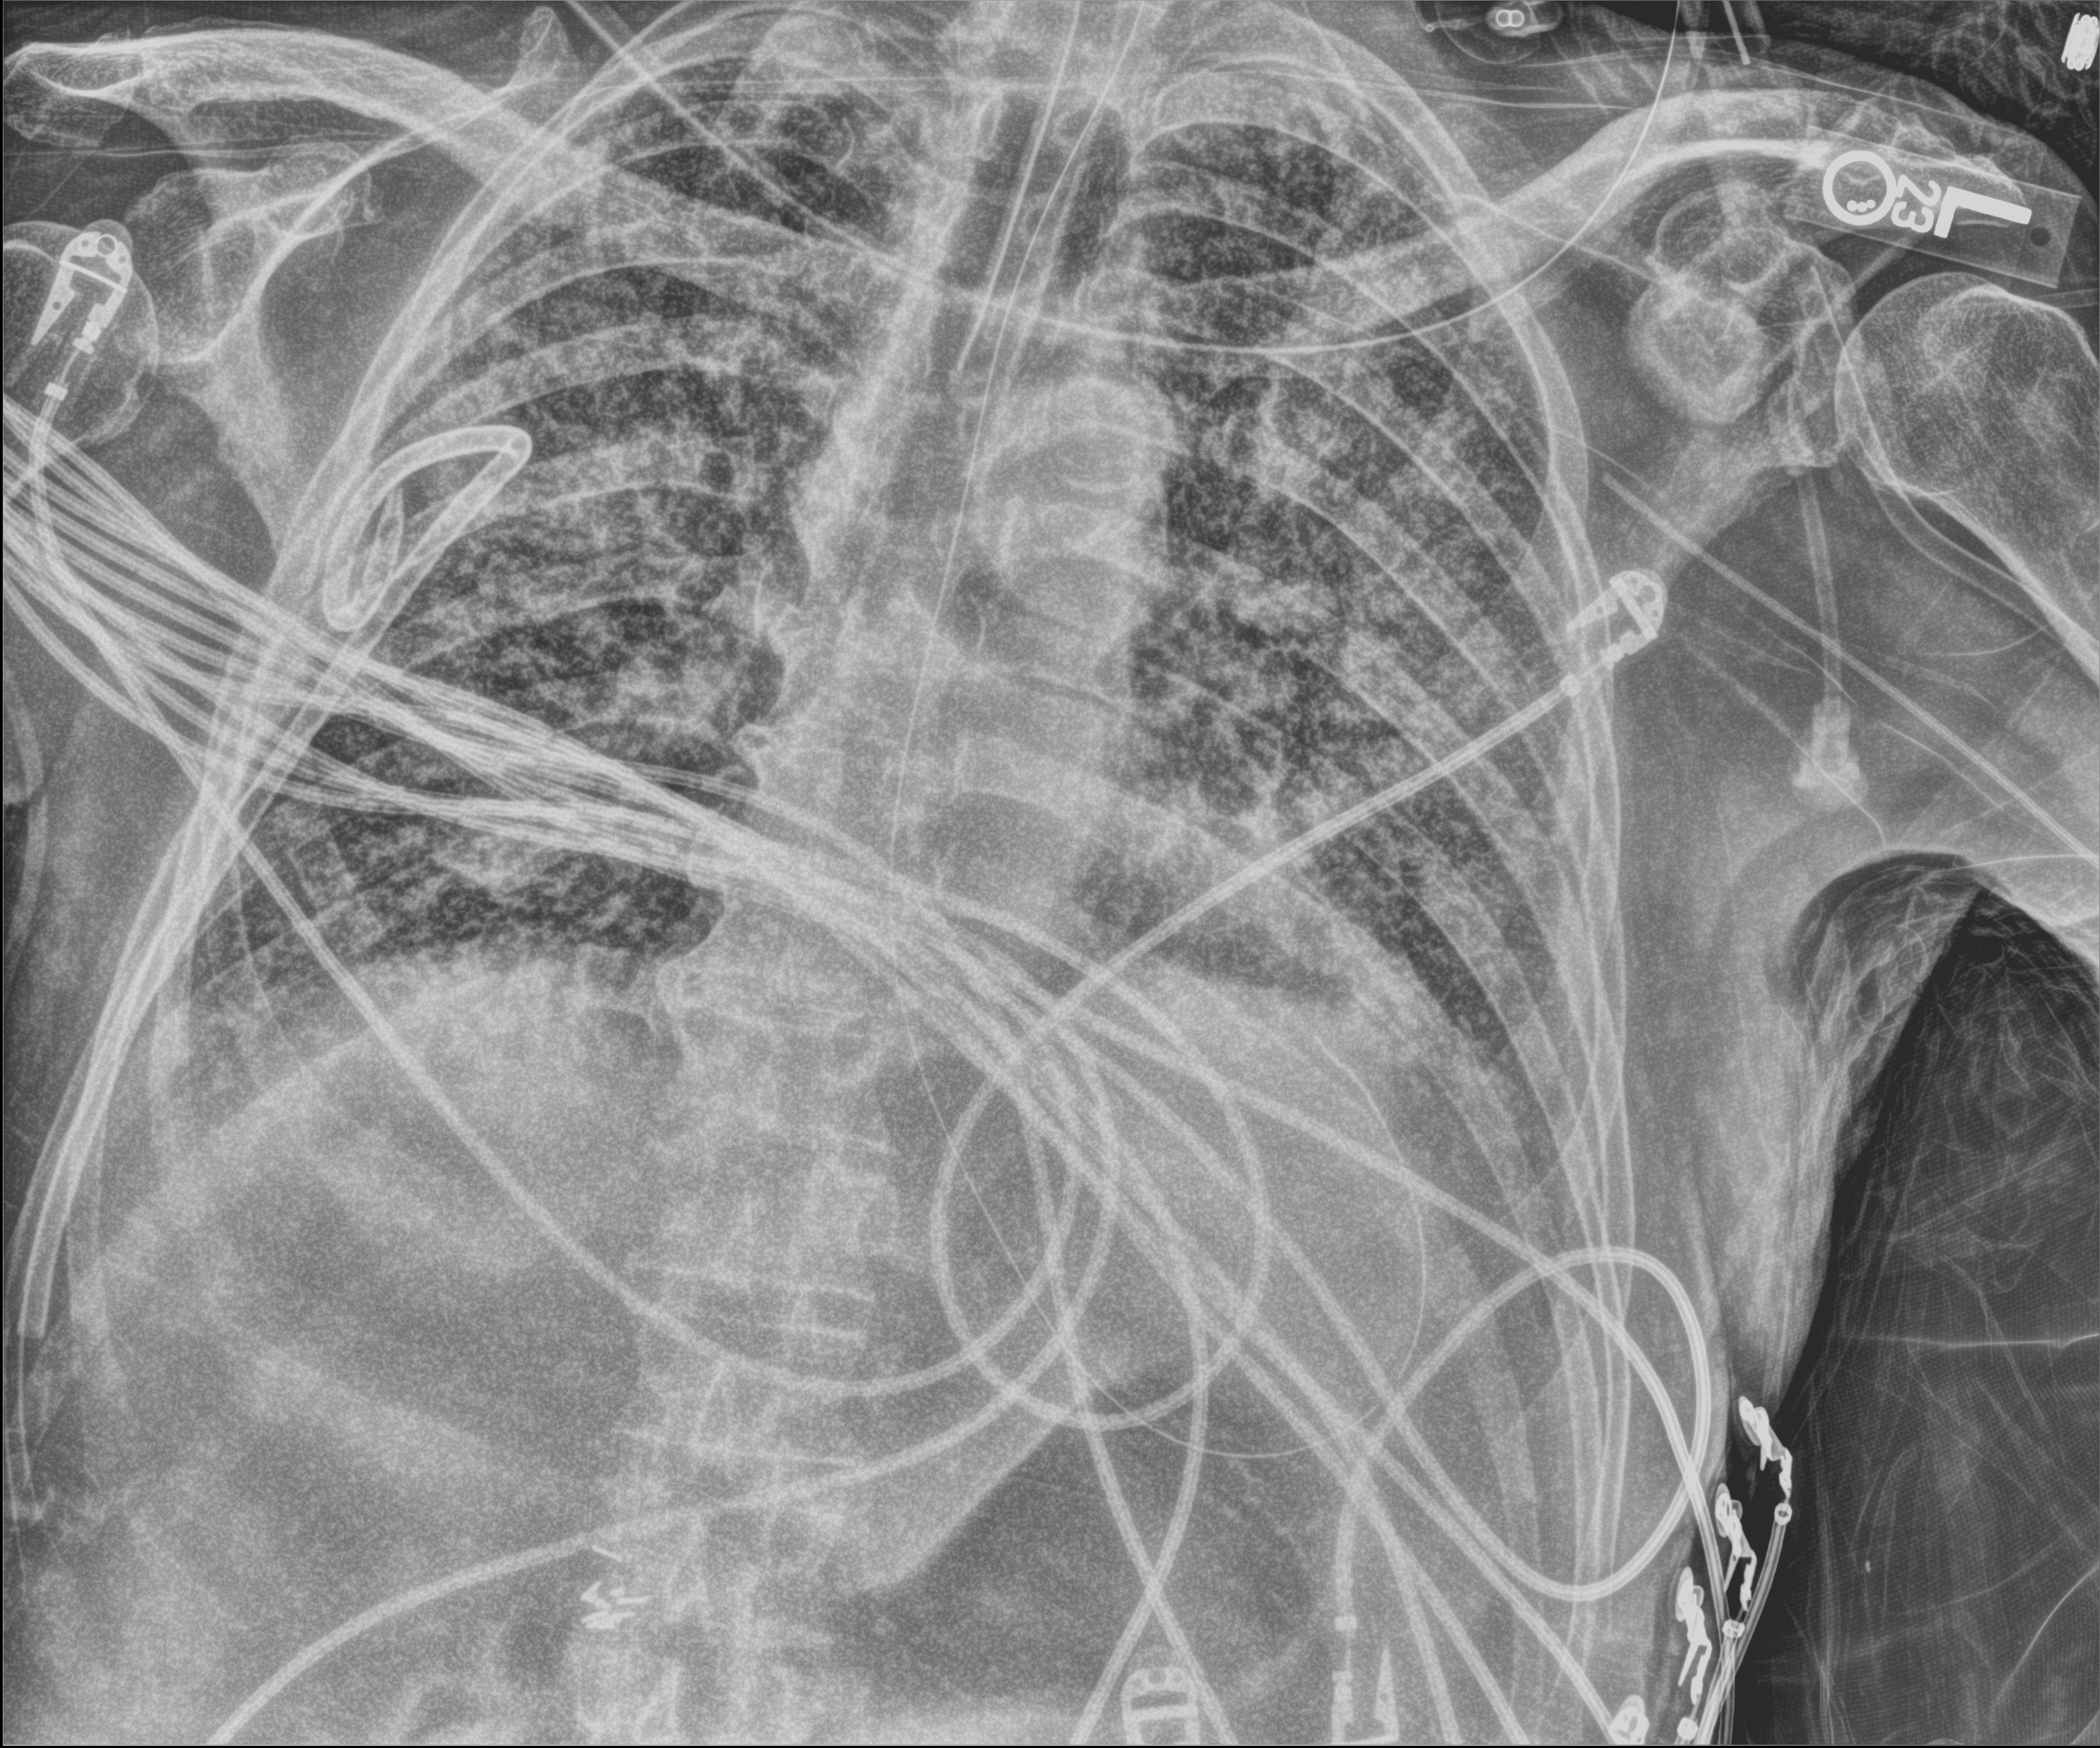
Chest X-ray (portable); anteroposterior (AP) projection. Male patient hospitalised with COVID-19, age 75–90 years.
Hospital-stay facts (about this admission, not read from this image; timing relative to this image not recorded):
- chronic kidney disease (admission record): no
- other chronic lung disease (admission record): no
- admitted to intensive care during this hospital stay: yes